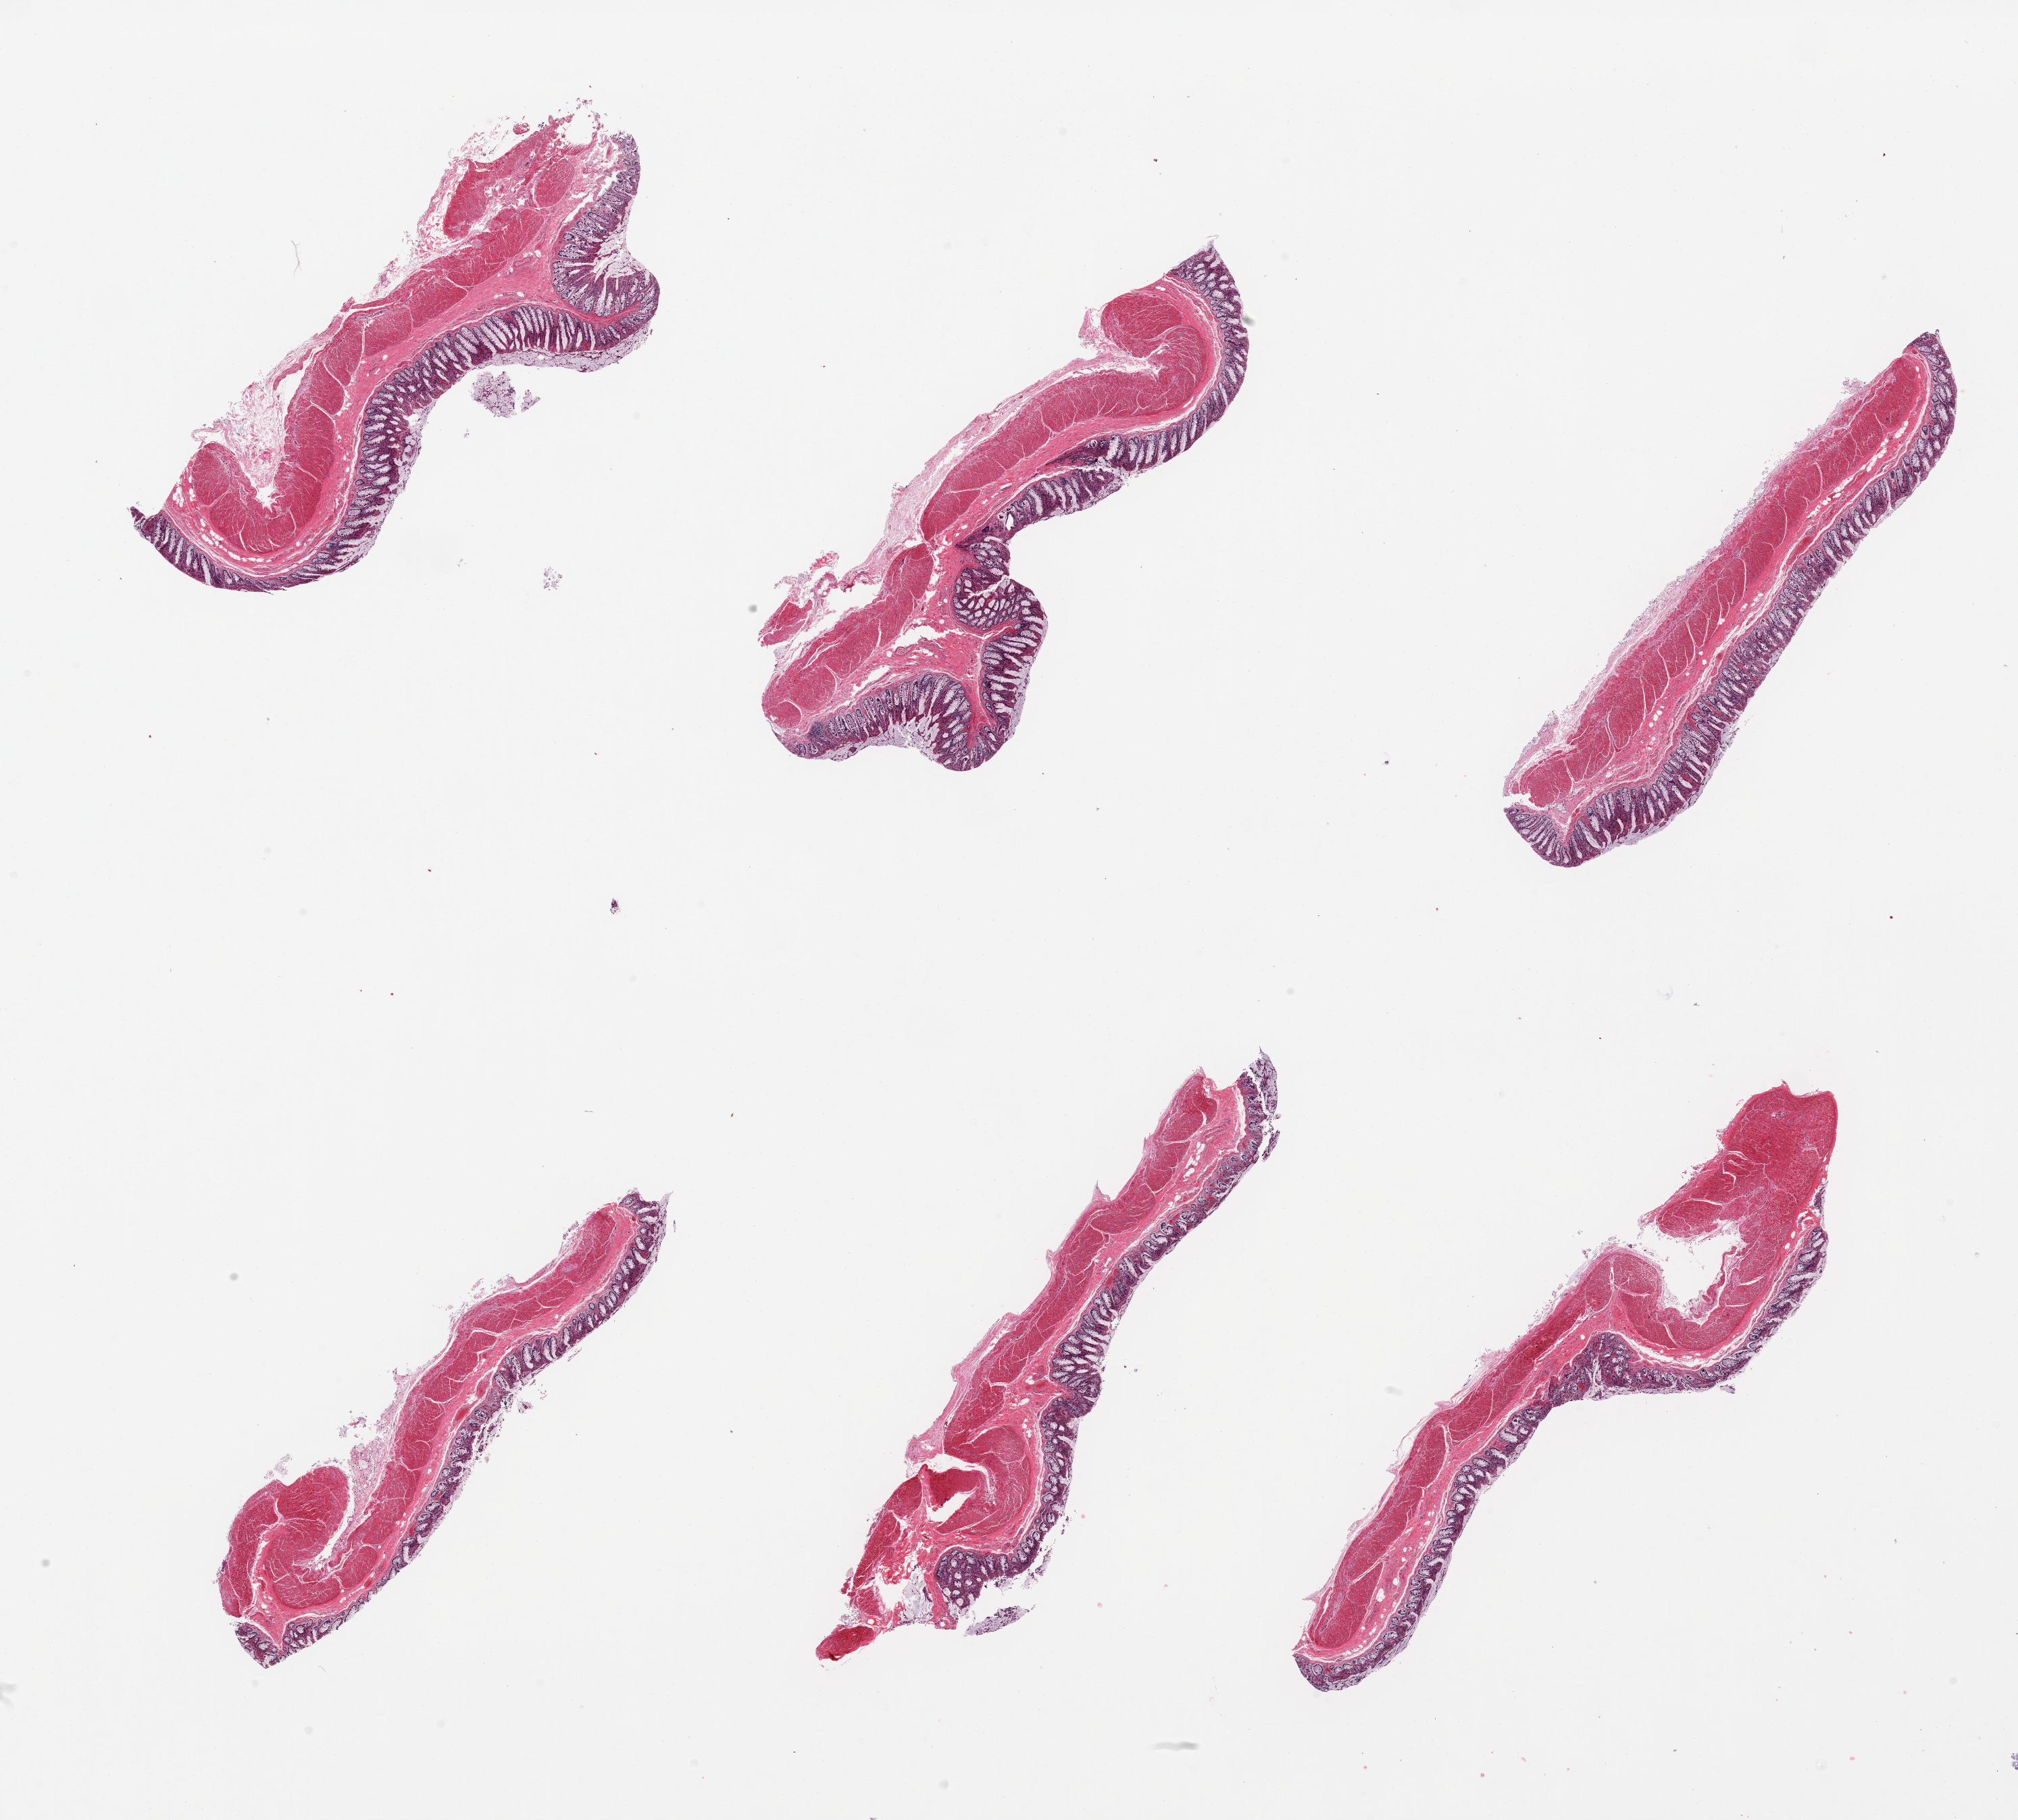
Digitized hematoxylin and eosin (H&E)-stained section, a low-resolution overview of the entire scanned area, about 23.6 x 21.3 mm (acquisition: 20x scan); PAXgene-fixed, paraffin-embedded tissue; sampled site (target tissue): transverse colon; tissue donor sample.
* review note (as recorded): 6 pieces, mucosa up to ~0.5mm, remarkably well preserved, focally approaches score 2